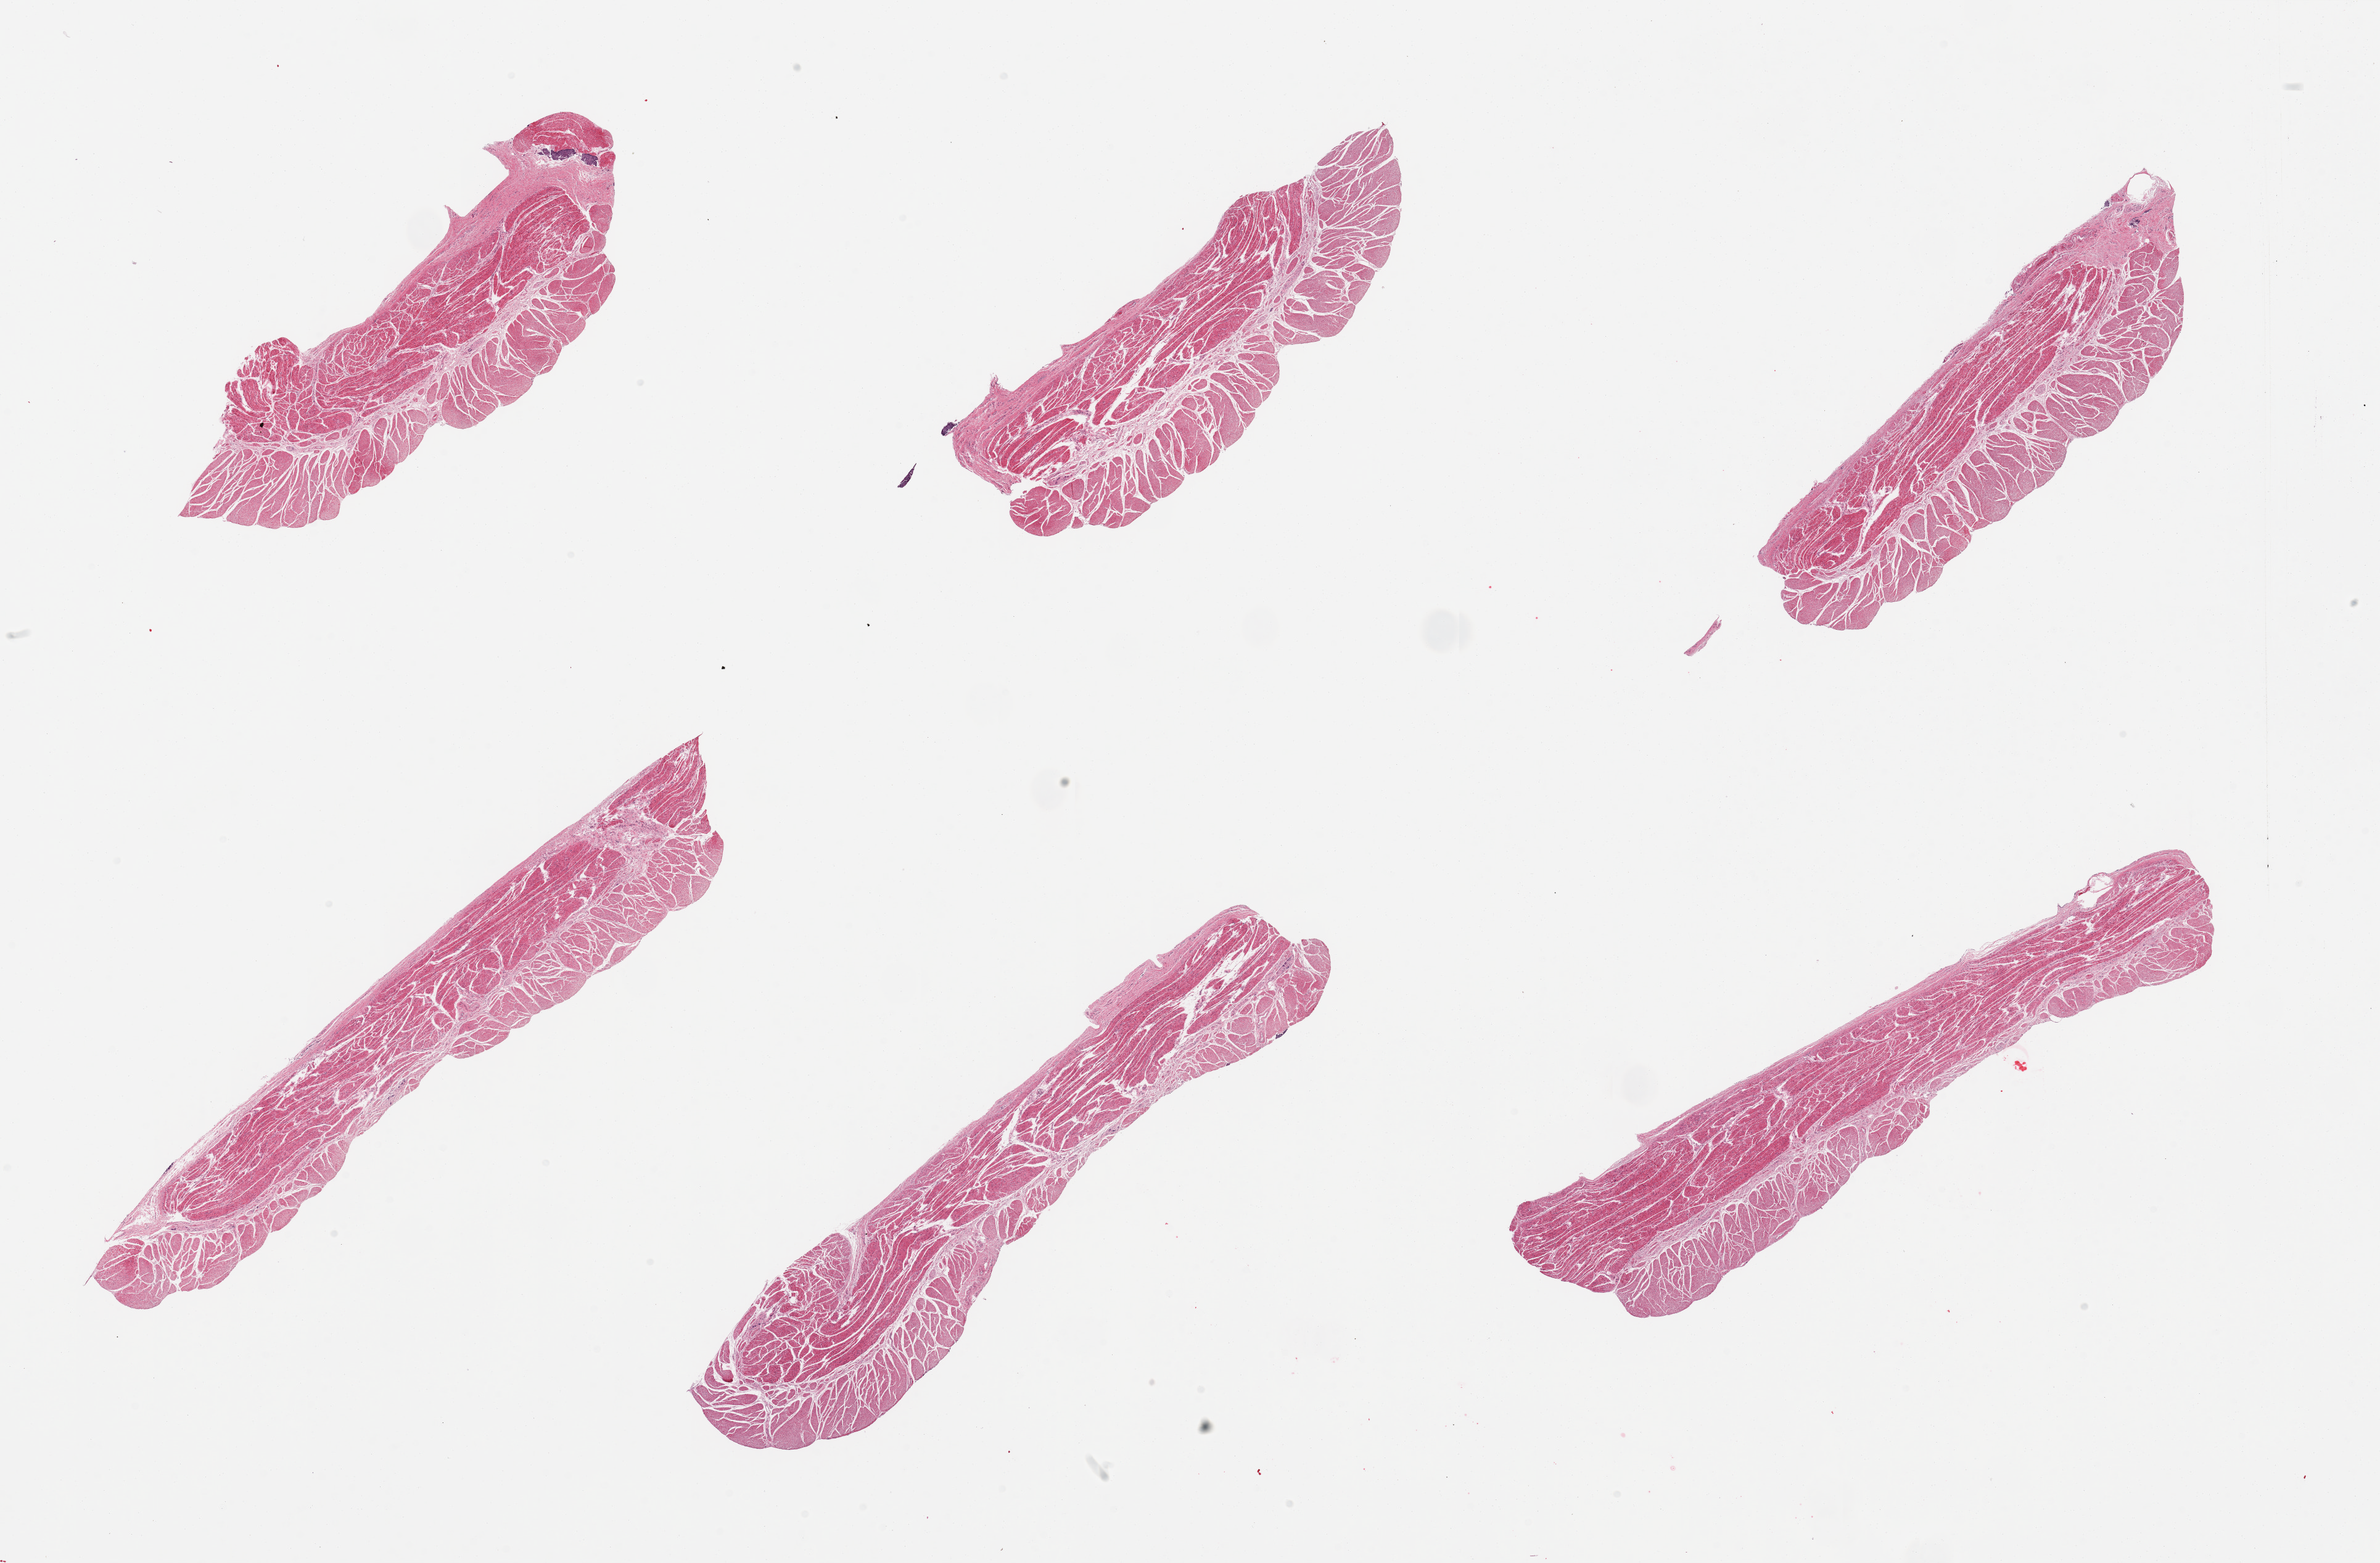
Whole-slide image, hematoxylin and eosin (H&E) stain, whole scanned area (about 30.5 x 20.0 mm, slide scanned at 20x) shown as a low-resolution overview, PAXgene-fixed, paraffin-embedded tissue, section of esophageal muscle (target tissue), donor tissue sample. Donor sex: male.
Review note (as recorded): 6 pieces, all target muscularis.